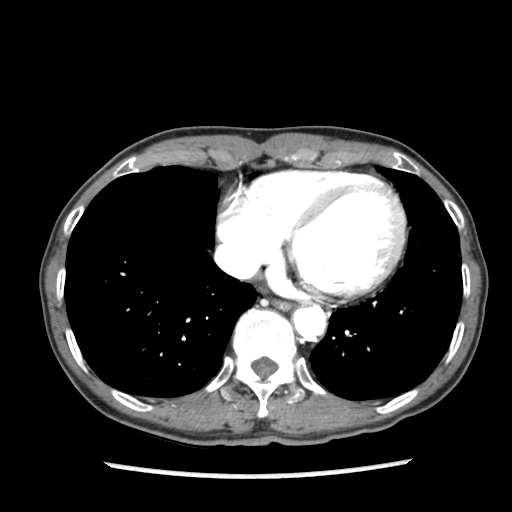
Contrast-enhanced abdominal CT (liver protocol), one axial slice; slice 81 of 87 in the series (ordered by position); reconstruction kernel STANDARD; 140 kVp; soft-tissue window (W 400 / L 40 HU); 2.5 mm slice thickness; 512 × 512 image matrix. Case-level facts recorded for this patient, not image findings: diagnosis: hepatocellular carcinoma (patient treated with transarterial chemoembolisation; whether this scan precedes or follows treatment is not stated here); TNM stage (as recorded): Stage-IIIB; Child-Pugh class: A.
Outlined on this slice (semi-automatically segmented with operator editing):
- abdominal aorta: bounding box (x1, y1, x2, y2) in pixels: (294, 306, 324, 340)